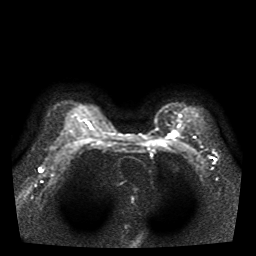
Breast MRI, one axial slice. Position 29 of 39 along the scan axis. Diffusion-weighted series; image 2 of 4 stored at this slice position (different b-values; order by instance number). 1.5 T. 5 mm slice thickness. 256 × 256 image matrix, field of view 330 × 330 mm. Female patient.
Annotated regions visible in this slice (expert manual segmentation):
- tumour on diffusion-weighted imaging: bounding box (x1, y1, x2, y2) in pixels: (167, 132, 178, 139)